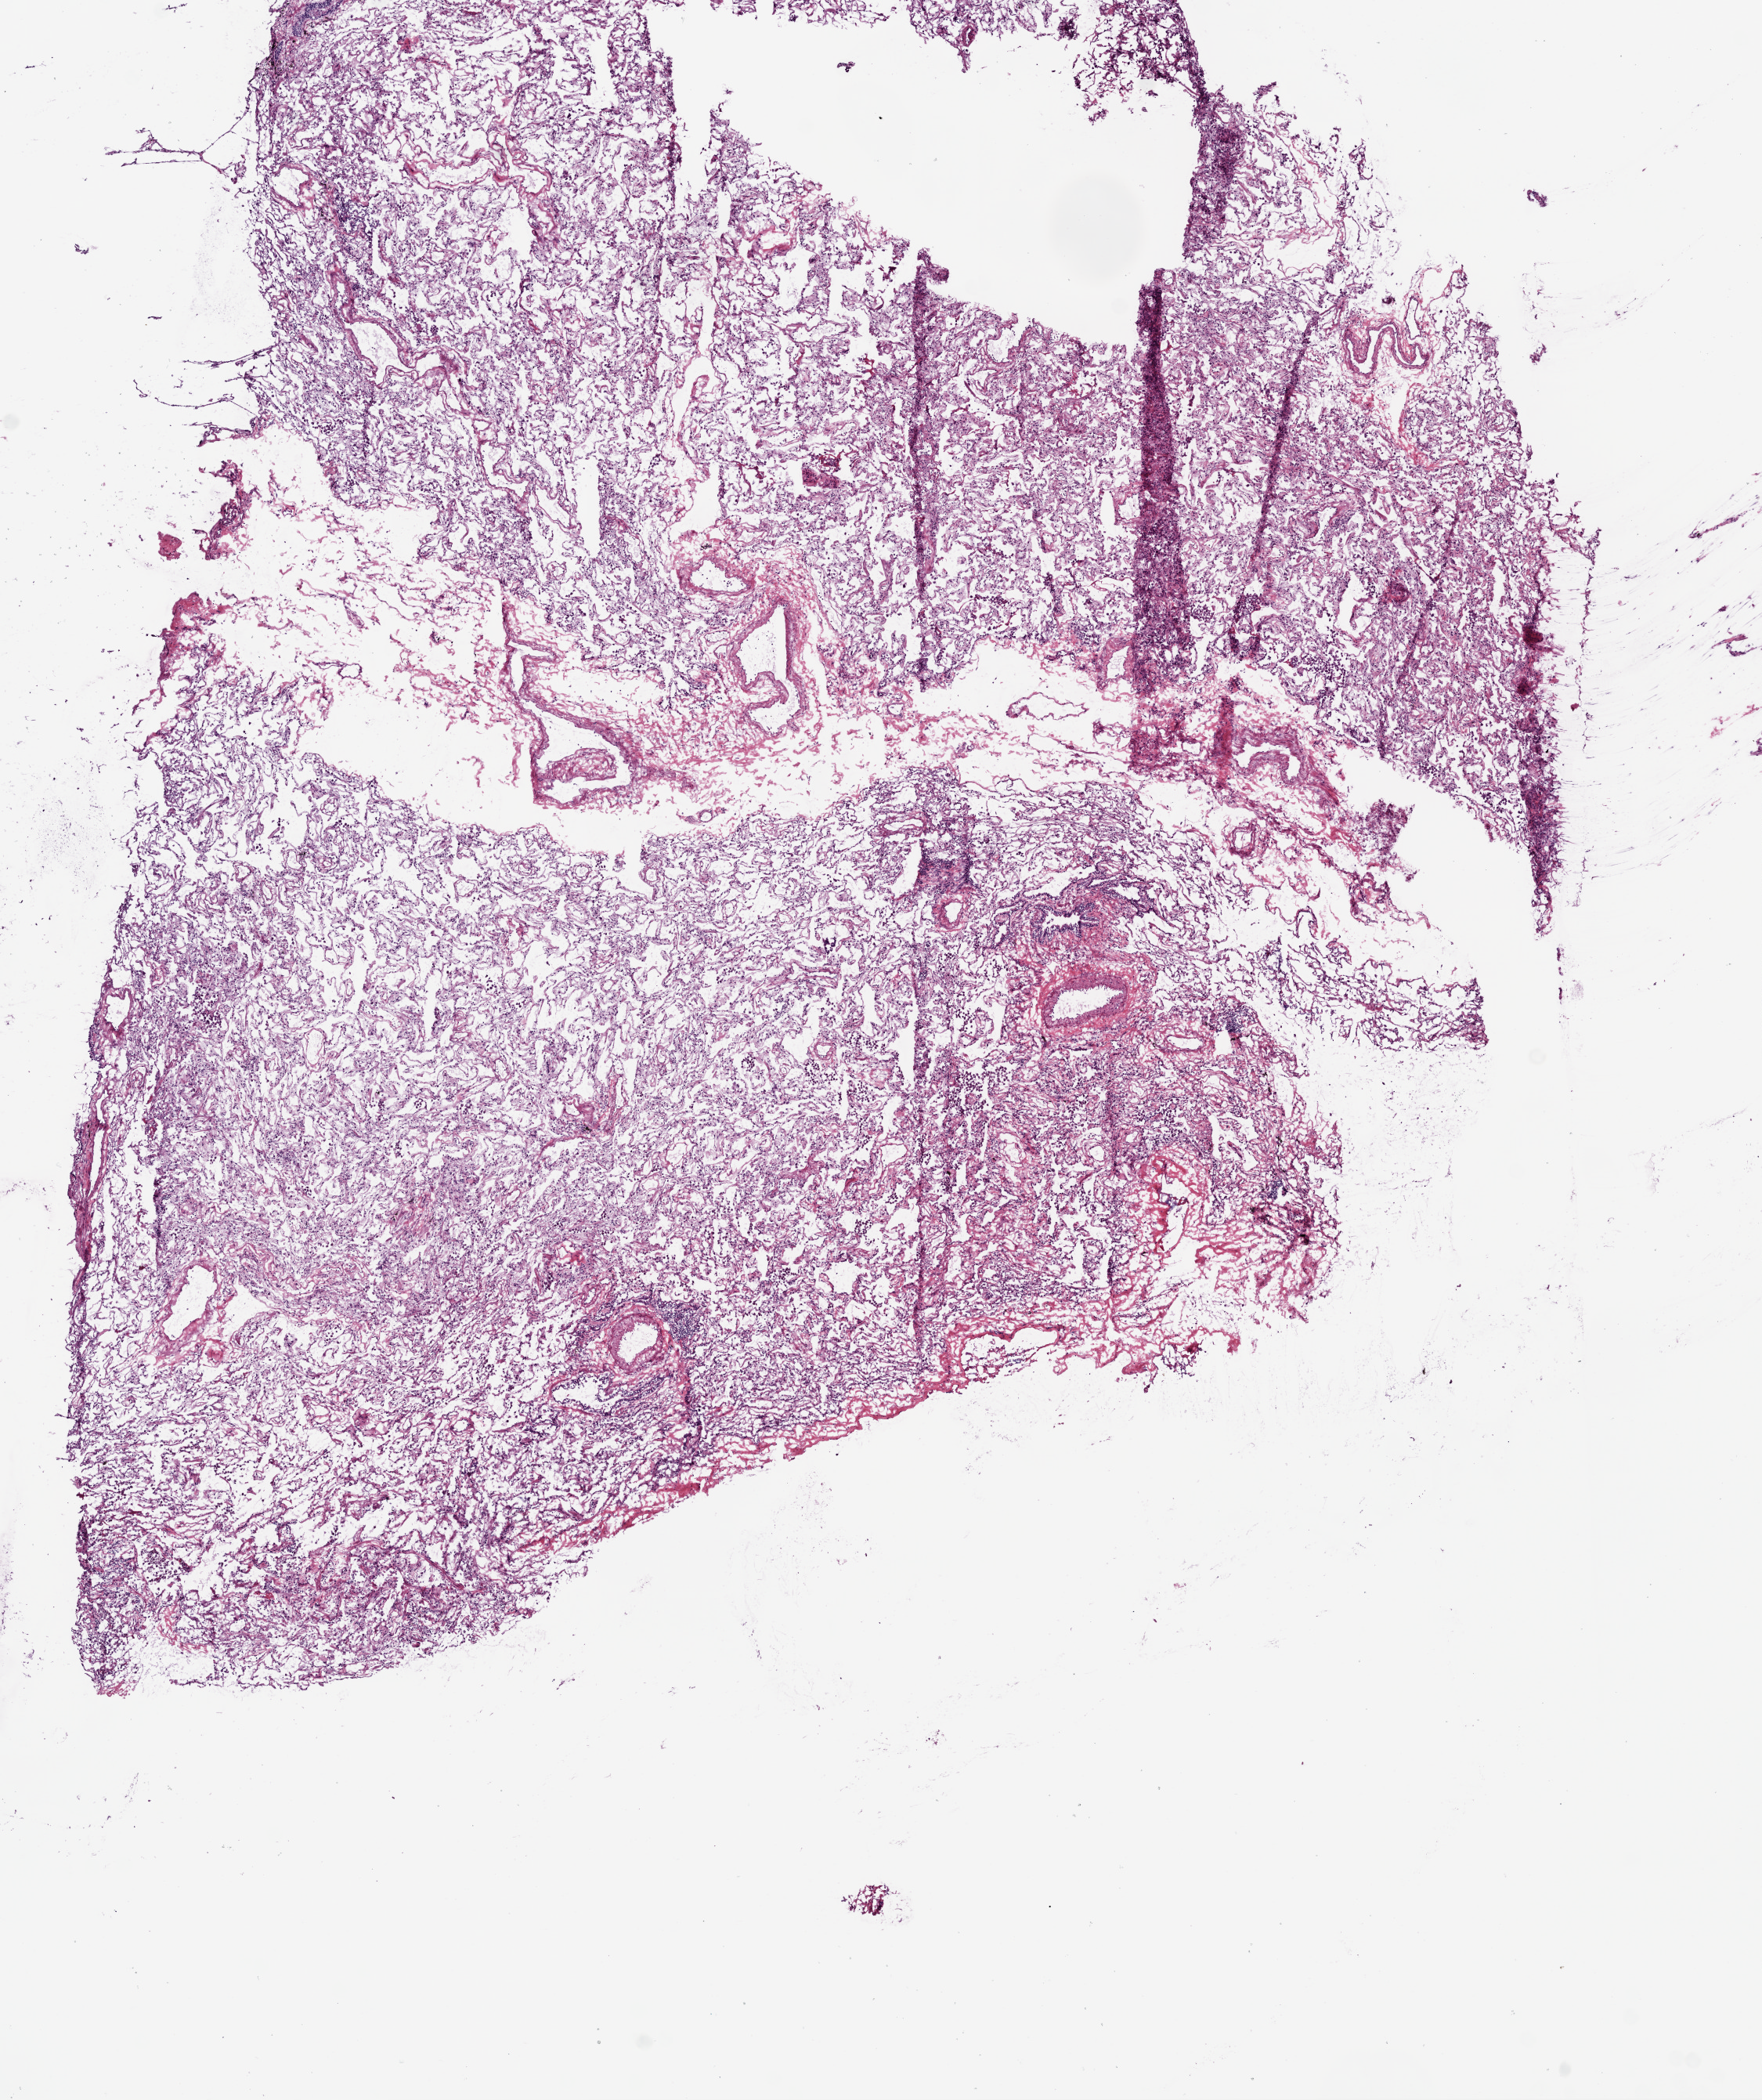
H&E-stained whole-slide image, shown as a low-resolution overview of the whole scanned area (about 9.0 x 10.8 mm, slide scanned at 20x). Frozen section from the bottom of the tissue portion. Lung, solid tissue normal (non-tumour tissue) sample. Female, age 75 years at initial diagnosis.
This section: solid tissue normal sample (biorepository sample class). Patient diagnosis: Papillary adenocarcinoma, NOS (upper lobe, lung).